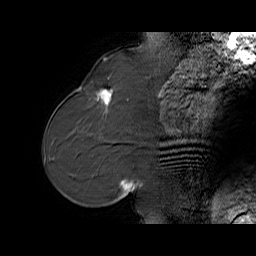
Breast MRI (dynamic contrast-enhanced), one sagittal slice. Slice 24 of 65 in the series (ordered by position). Dynamic contrast-enhanced series, time point 2 of 6 at this slice position (early post-contrast). 1.5 T. TE 5.7 ms, TR 32.9 ms. 4 mm slice thickness. 256 × 256 image matrix, field of view 230 × 230 mm. Female patient. From the clinical record (not read from this slice): setting: breast cancer imaged before/during neoadjuvant chemotherapy; receptor status: HER2-positive.
Outlined on this slice (semi-automatic segmentation, software-assisted and operator-edited):
- analysis volume of interest (the breast-tissue region the enhancement analysis was run in; not a lesion): bounding box [x1, y1, x2, y2] px = [76, 77, 125, 128]
- tumour enhancement mask (voxels above the 100 % enhancement threshold inside the analysis volume of interest): [95, 89, 113, 112]